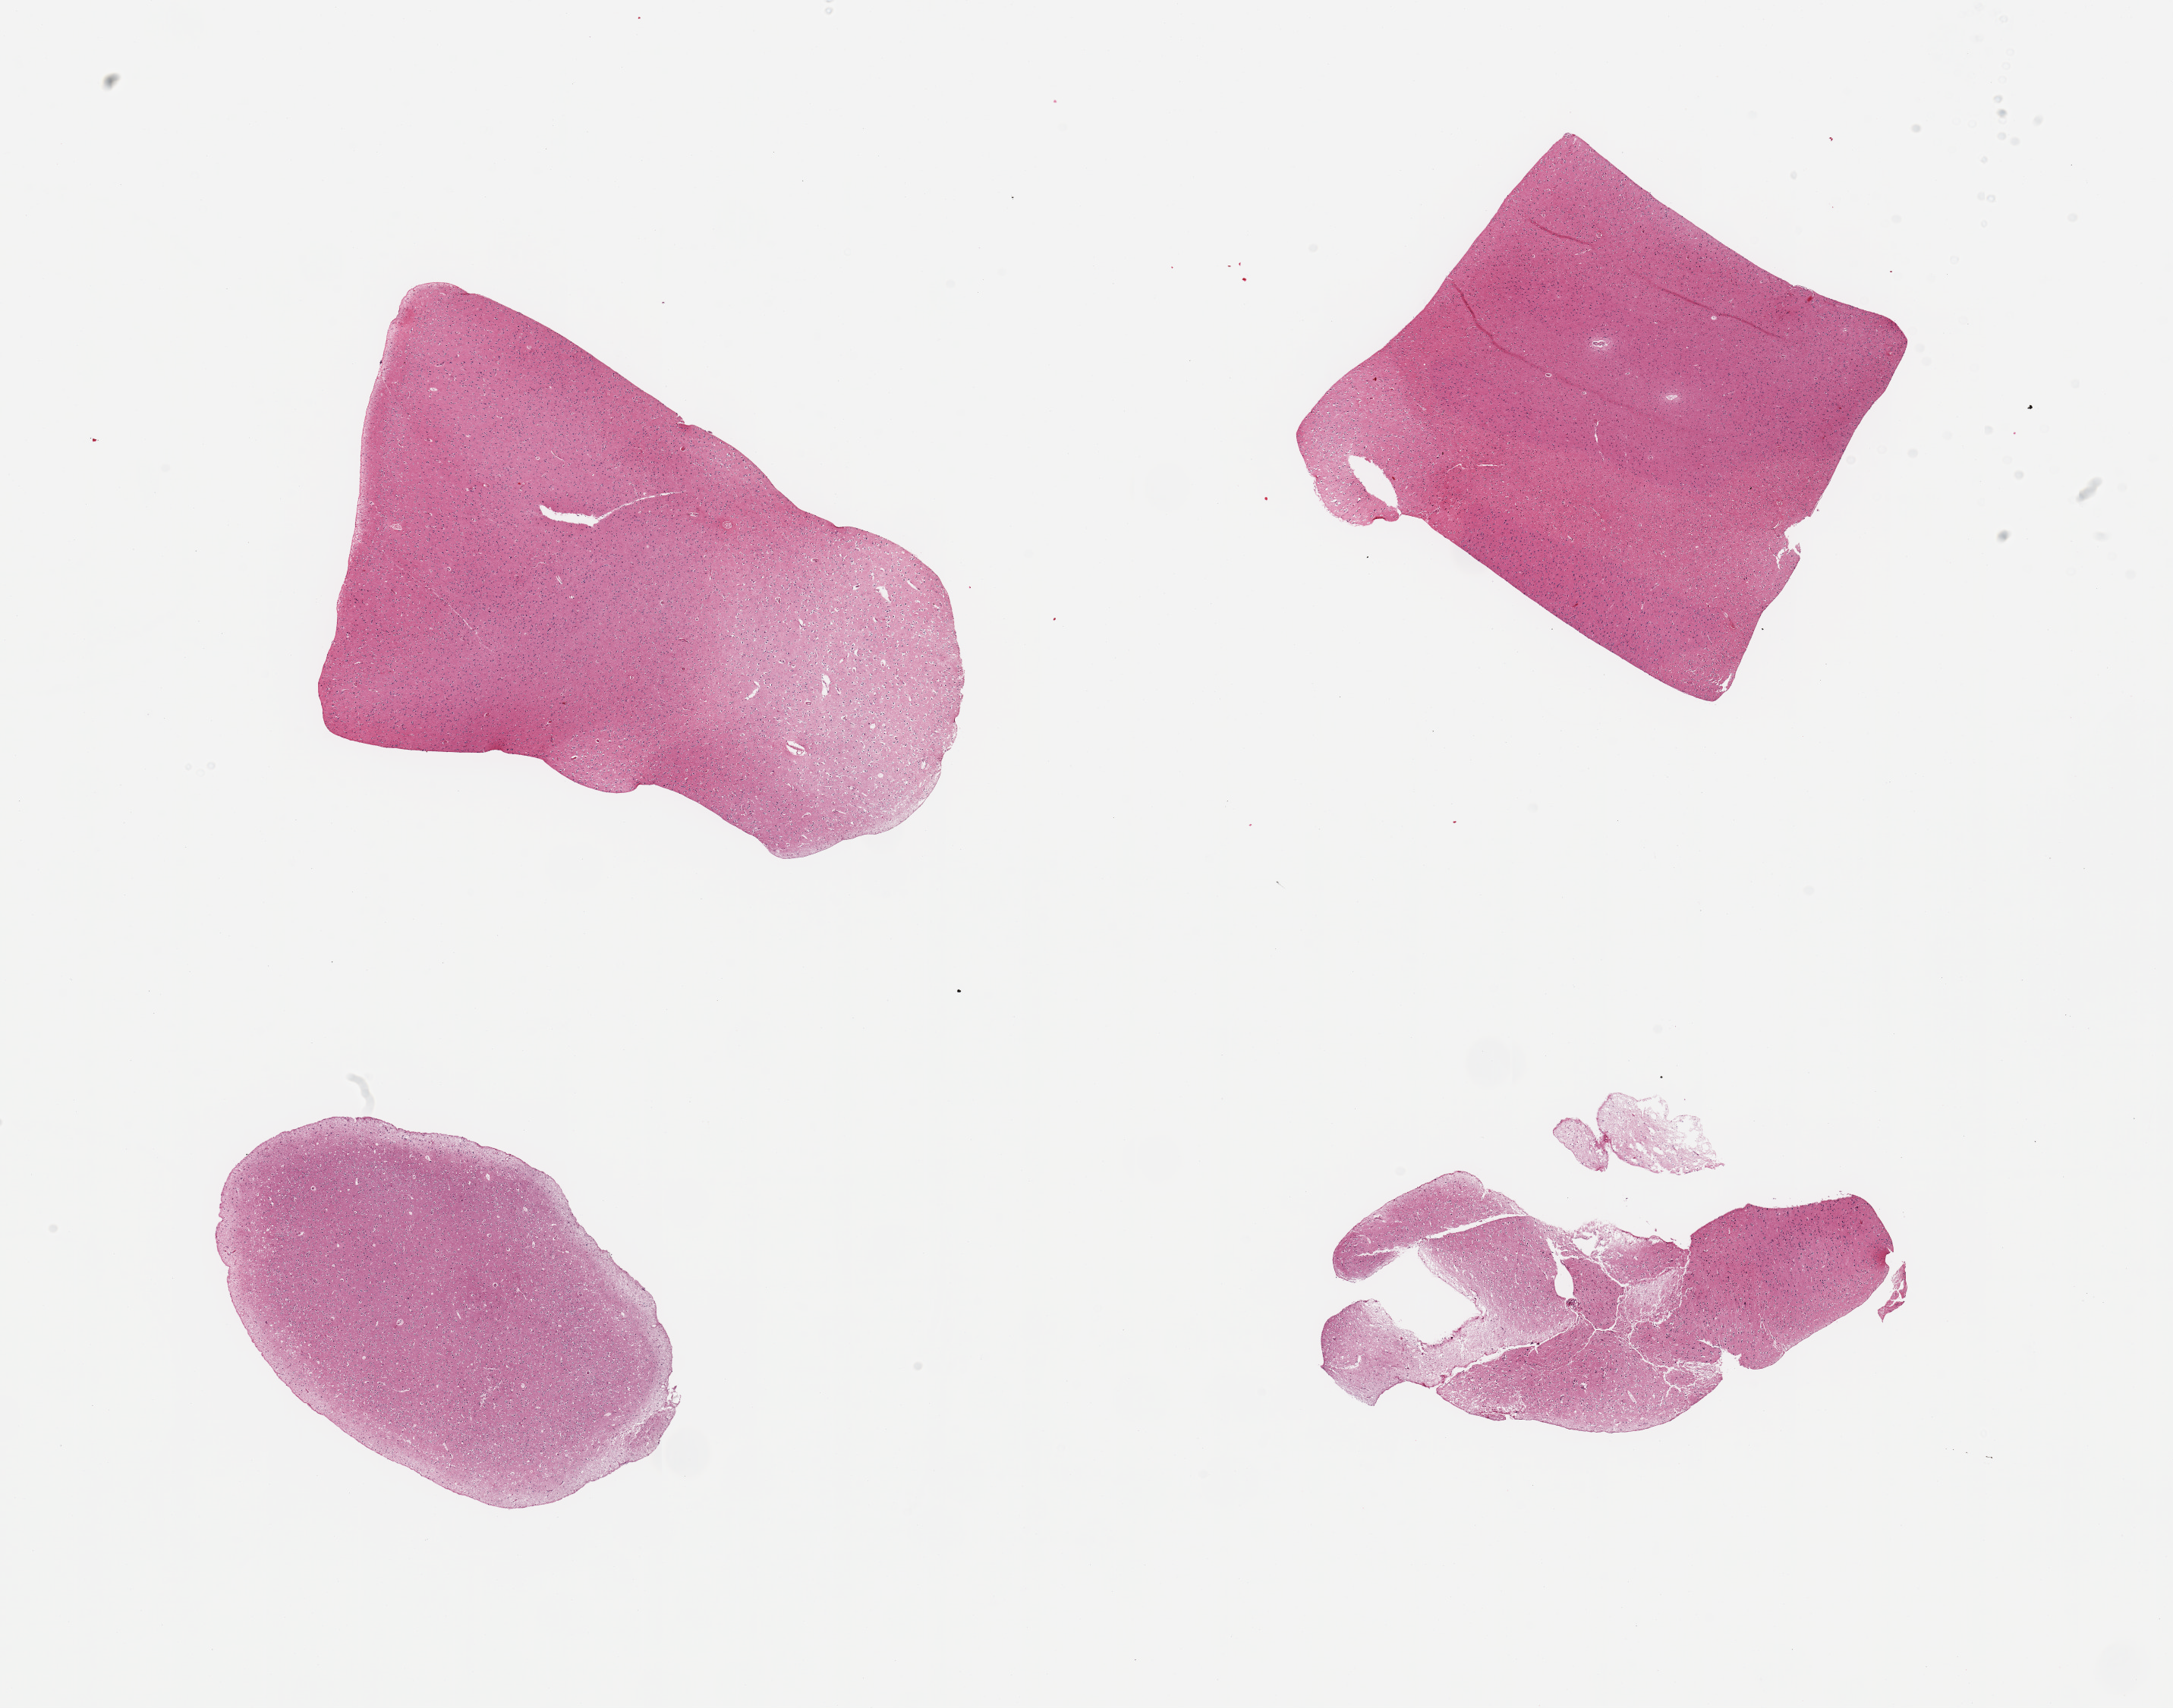
Digitized haematoxylin and eosin-stained section, brightfield — low-resolution overview of the scanned area, about 22.6 x 17.8 mm (acquisition: 20x scan). PAXgene-fixed, paraffin-embedded tissue. Section of cerebral cortex (target tissue). Donor tissue sample.
Review note (as recorded): 4 pieces.